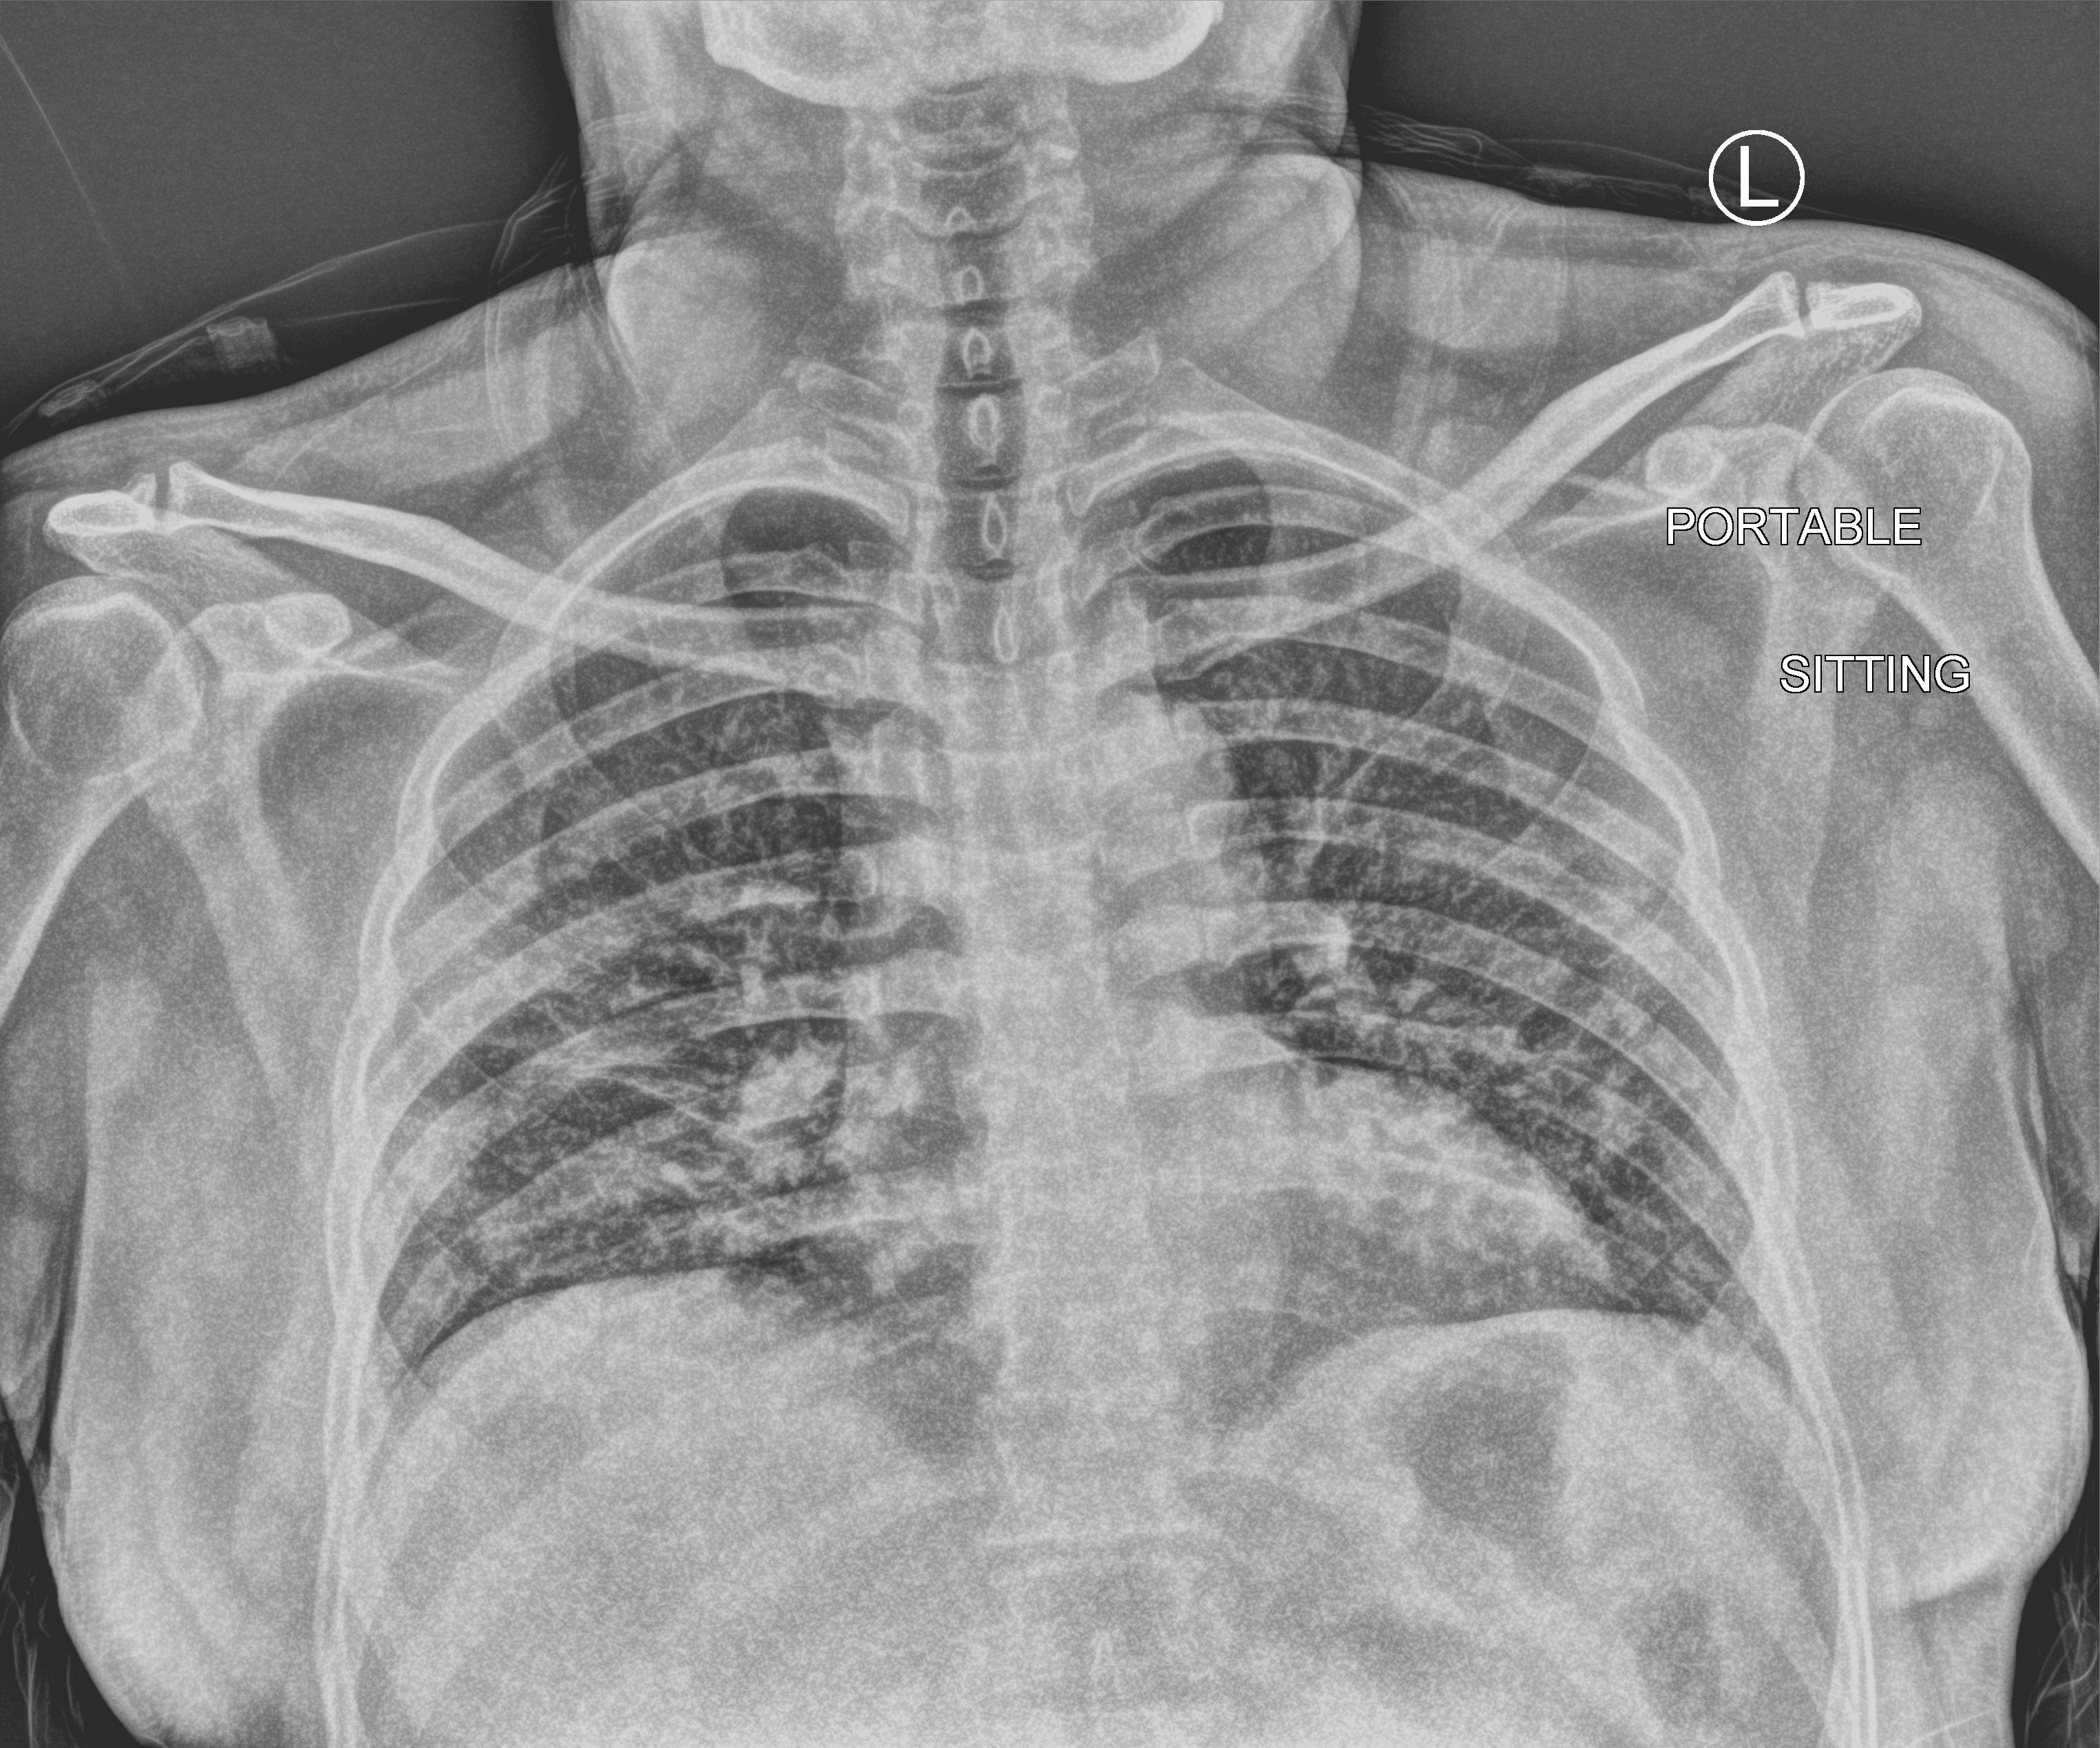
Chest X-ray (portable). Patient hospitalised with COVID-19; male, aged 18–59 years.
Hospital-stay facts (about this admission, not read from this image; timing relative to this image not recorded):
- other chronic lung disease (admission record): no
- mechanically ventilated during this hospital stay: no